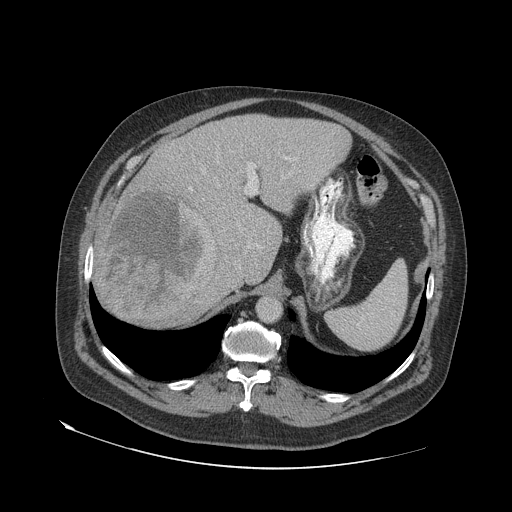
Contrast-enhanced abdominal CT (liver protocol), one axial slice. Slice 49 of 79 in the series (ordered by position). Reconstruction kernel STANDARD. 140 kVp. Soft-tissue window (W 400 / L 40 HU). 512 × 512 image matrix, field of view 480 × 480 mm. Case-level facts recorded for this patient, not image findings: diagnosis: hepatocellular carcinoma (patient treated with transarterial chemoembolisation; whether this scan precedes or follows treatment is not stated here); TNM stage (as recorded): Stage-IVA; Child-Pugh class: A; tumour differentiation: well differentiated.
Annotated regions visible in this slice (semi-automatic segmentation, software-assisted and operator-edited):
- liver parenchyma outside the tumour (the mass and vessels are separate outlines, so this box may not span the whole liver): box from (x=96, y=114) to (x=350, y=320) px
- mass: (x=100, y=191)–(x=219, y=324)
- liver vessels: (x=189, y=156)–(x=296, y=248)